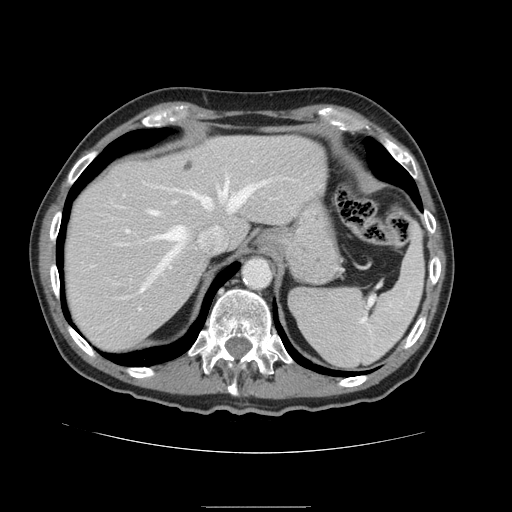
Contrast-enhanced abdominal CT, one axial slice; slice 120 of 168 in the series (ordered by position); intravenous contrast given; soft-tissue window (W 400 / L 40 HU); 2.5 mm slice thickness; 512 × 512 image matrix, field of view 386 × 386 mm. Male patient, age 74 years. Case-level facts recorded for this patient, not image findings: diagnosis: colorectal cancer liver metastases, imaged before liver resection; multiple liver metastases: no; largest metastasis: 14.5 cm.
Structures marked on this image (expert manual segmentation):
- hepatic veins: bounding box (x1, y1, x2, y2) in pixels: (139, 179, 294, 293)
- liver: (64, 136, 327, 353)
- planned liver remnant (the part of the liver to remain after resection): (64, 136, 326, 352)